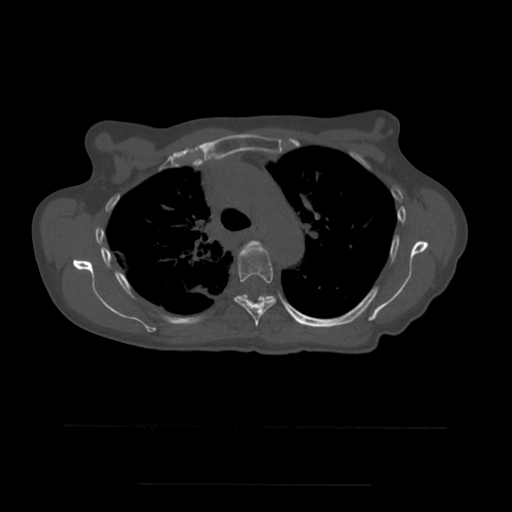
CT including the spine, one axial slice; position 391 of 544 along the scan axis; bone window (W 1800 / L 400 HU); 1.25 mm slice thickness; 512 × 512 image matrix, field of view 350 × 350 mm. Patient age 58 years. From the clinical record (not read from this slice): primary cancer: lung.
Outlined on this slice (semi-automatic segmentation, software-assisted and operator-edited):
- T4 vertebra: box from (x=240, y=241) to (x=267, y=254) px
- T5 vertebra: (x=234, y=247)–(x=276, y=327)
- T6 vertebra: (x=237, y=295)–(x=273, y=303)